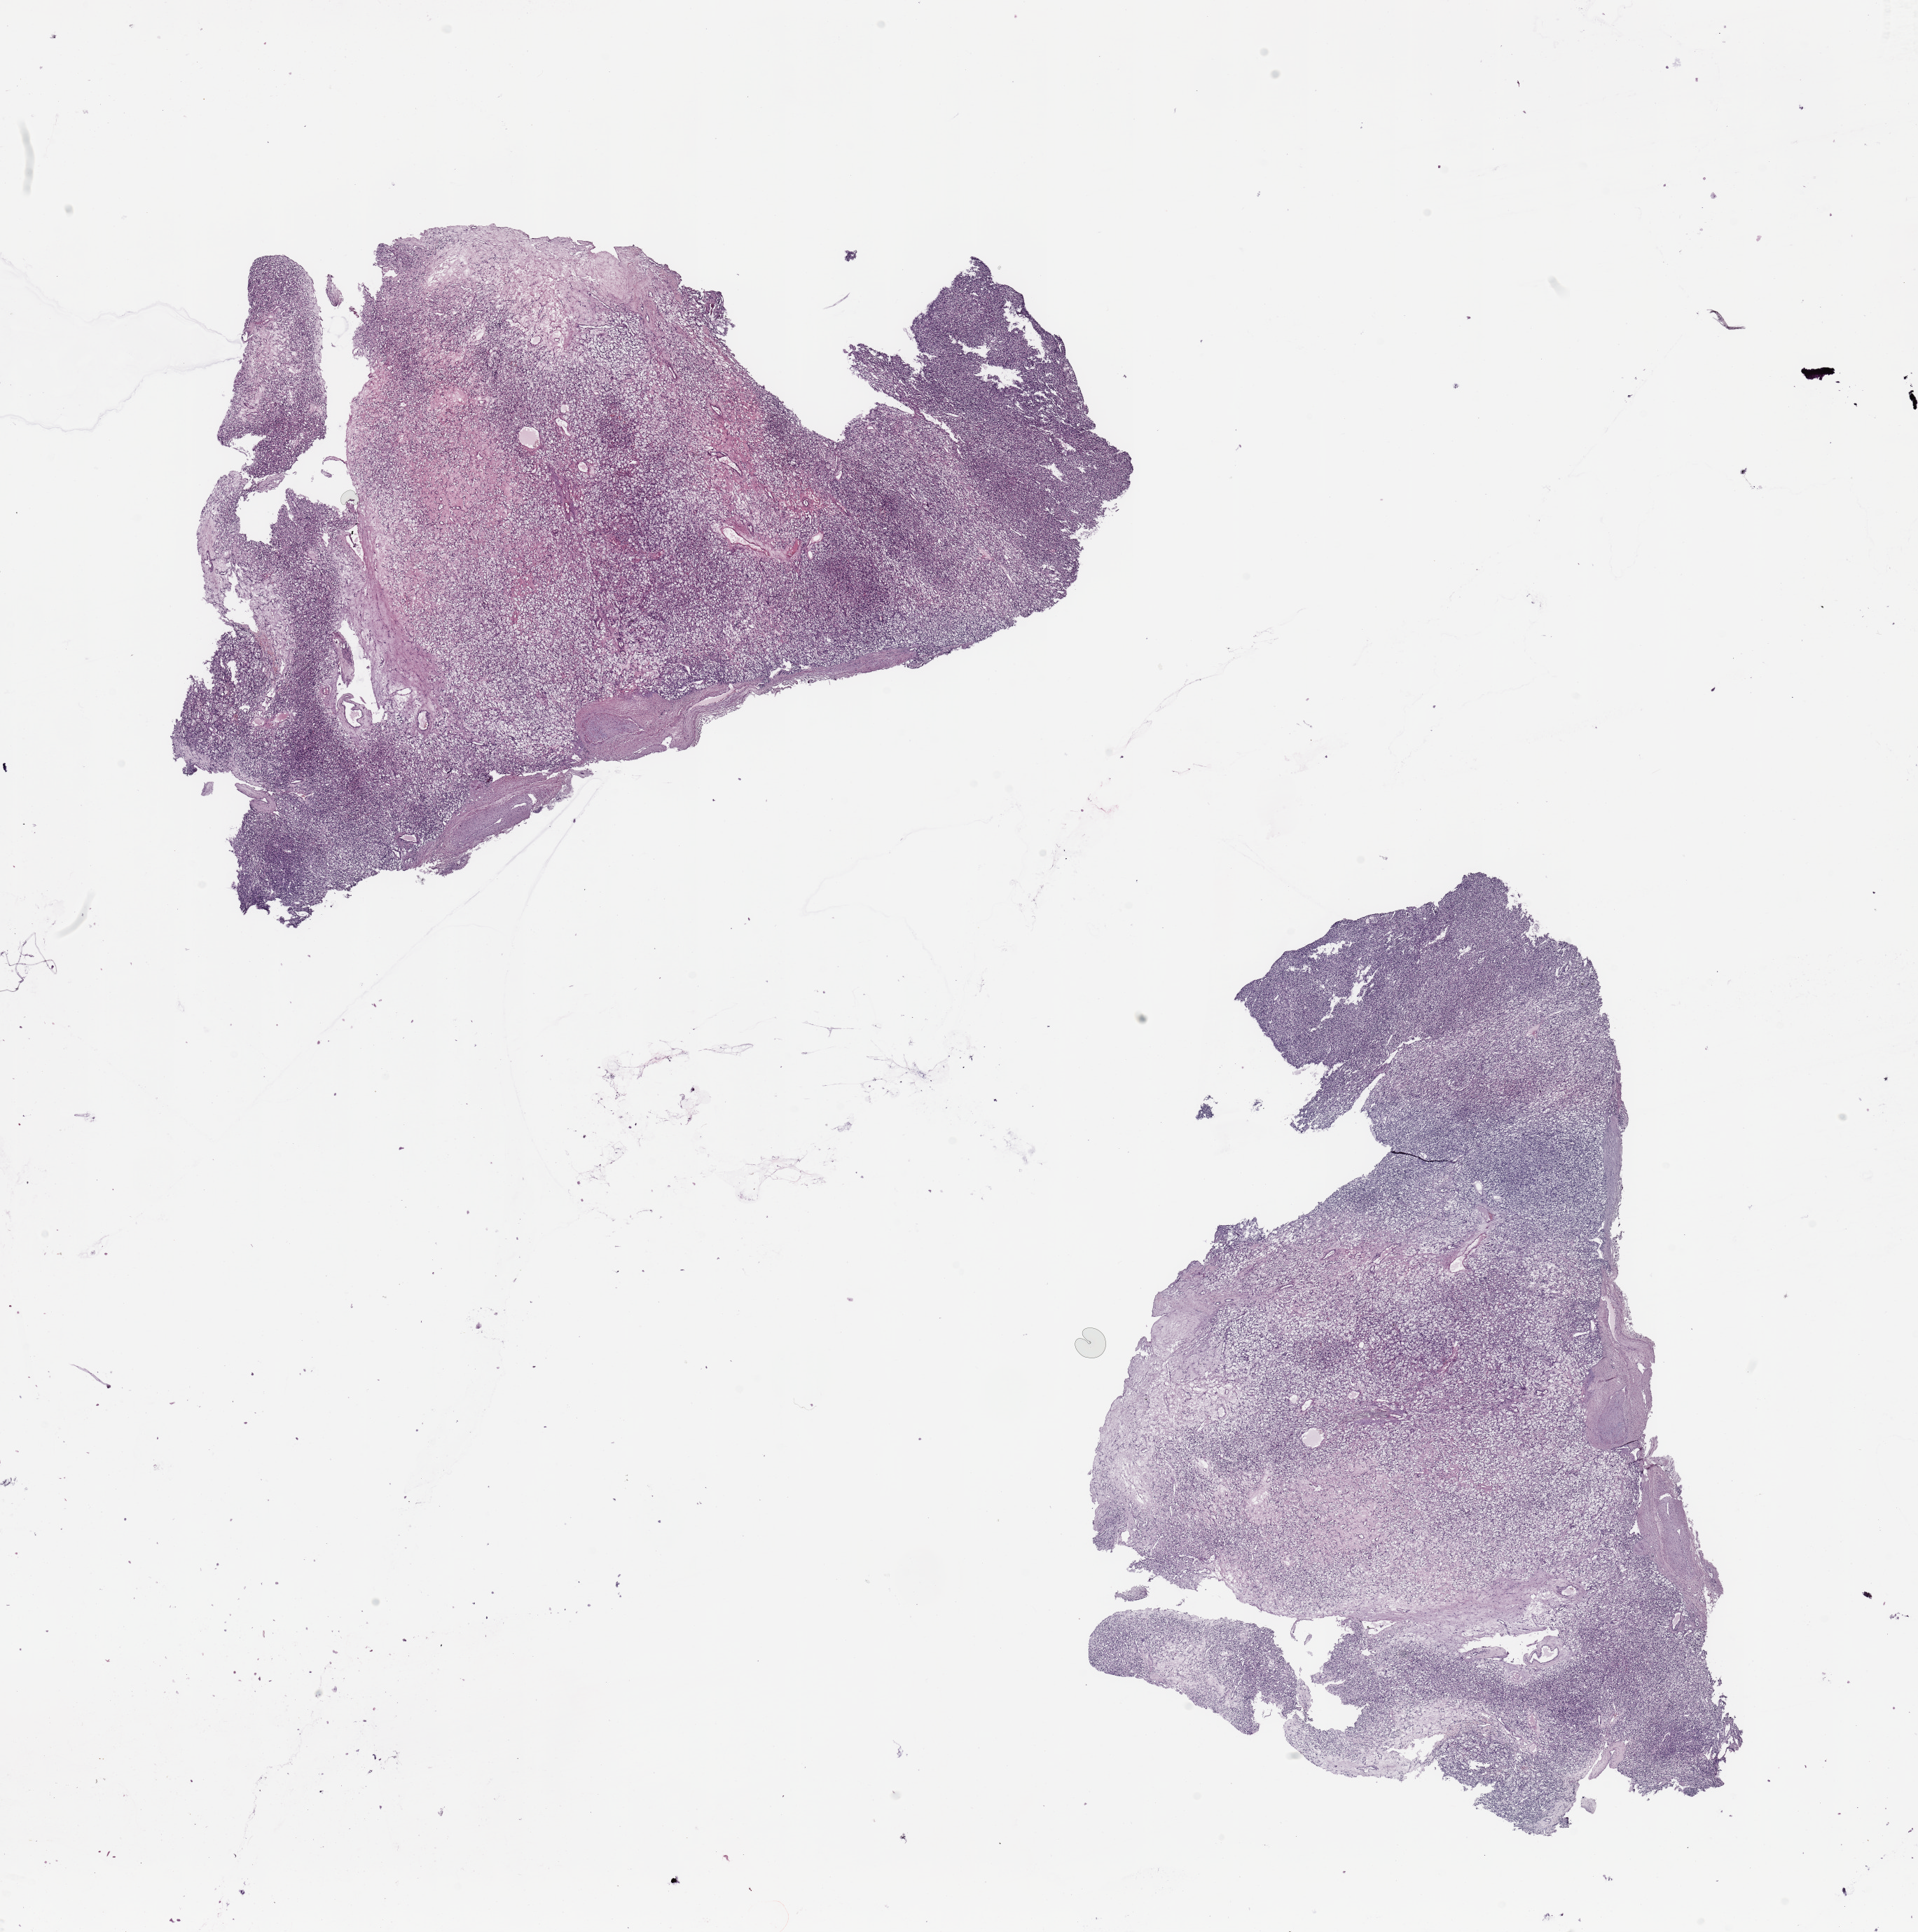
Digitized H&E-stained tissue section (whole slide) — shown as a low-resolution overview of the whole scanned area (about 21.7 x 21.8 mm, slide scanned at 20x), tumour tissue sample, kidney. Patient: female, age 66 years. Histologic grade: G2 (moderately differentiated).
Diagnosis: Renal cell carcinoma, NOS. Primary tumour site (as recorded): upper pole. AJCC pathologic stage: III.